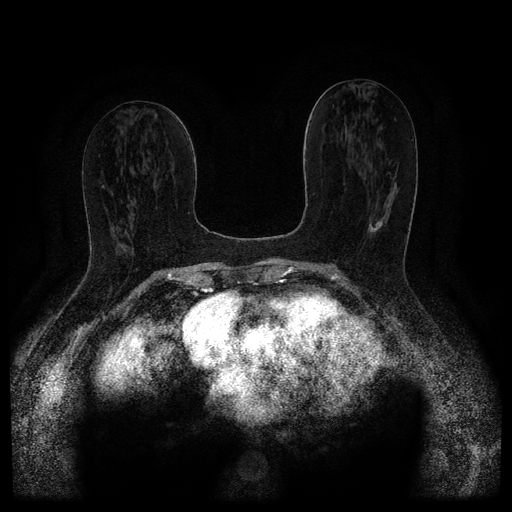
Breast MRI (dynamic contrast-enhanced, multi-phase), one axial slice. Position 50 of 116 along the scan axis. Dynamic contrast-enhanced series, time point 2 of 5 at this slice position (early post-contrast). 1.5 T. TE 2.6 ms, TR 5.4 ms. 2 mm slice thickness. 512 × 512 image matrix, field of view 340 × 340 mm. Female patient, age 67 years.
Outlined on this slice (semi-automatically segmented with operator editing):
- breast lesion (labelled 'tumour' in the annotation; benign lesions carry a separate 'benign' label): bounding box <367,218,384,233> (left, top, right, bottom; pixels)